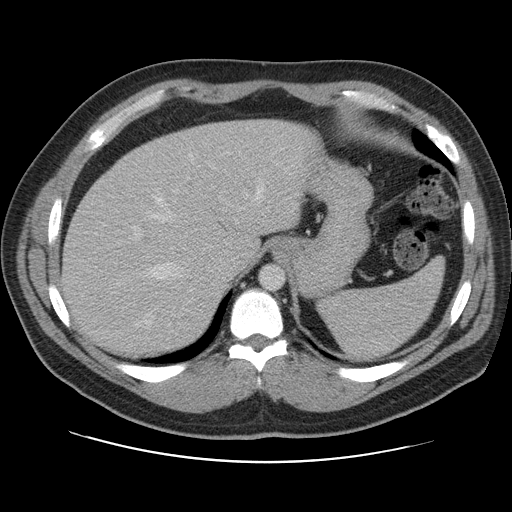
Contrast-enhanced abdominal CT, one axial slice; slice 84 of 109 in the series (ordered by position); 120 kVp; intravenous contrast given; soft-tissue window (W 400 / L 40 HU); 512 × 512 image matrix, field of view 402 × 402 mm. Male patient, age 35 years. From the clinical record (not read from this slice): diagnosis: colorectal cancer liver metastases, imaged before liver resection; multiple liver metastases: yes; largest metastasis: 2.8 cm; disease in both lobes: yes.
Structures marked on this image (manually delineated by an expert):
- hepatic veins: bounding box <144,179,265,324> (left, top, right, bottom; pixels)
- liver: <63,119,314,356>
- planned liver remnant (the part of the liver to remain after resection): <63,120,306,355>
- portal vein (with intrahepatic branches): <116,160,220,246>